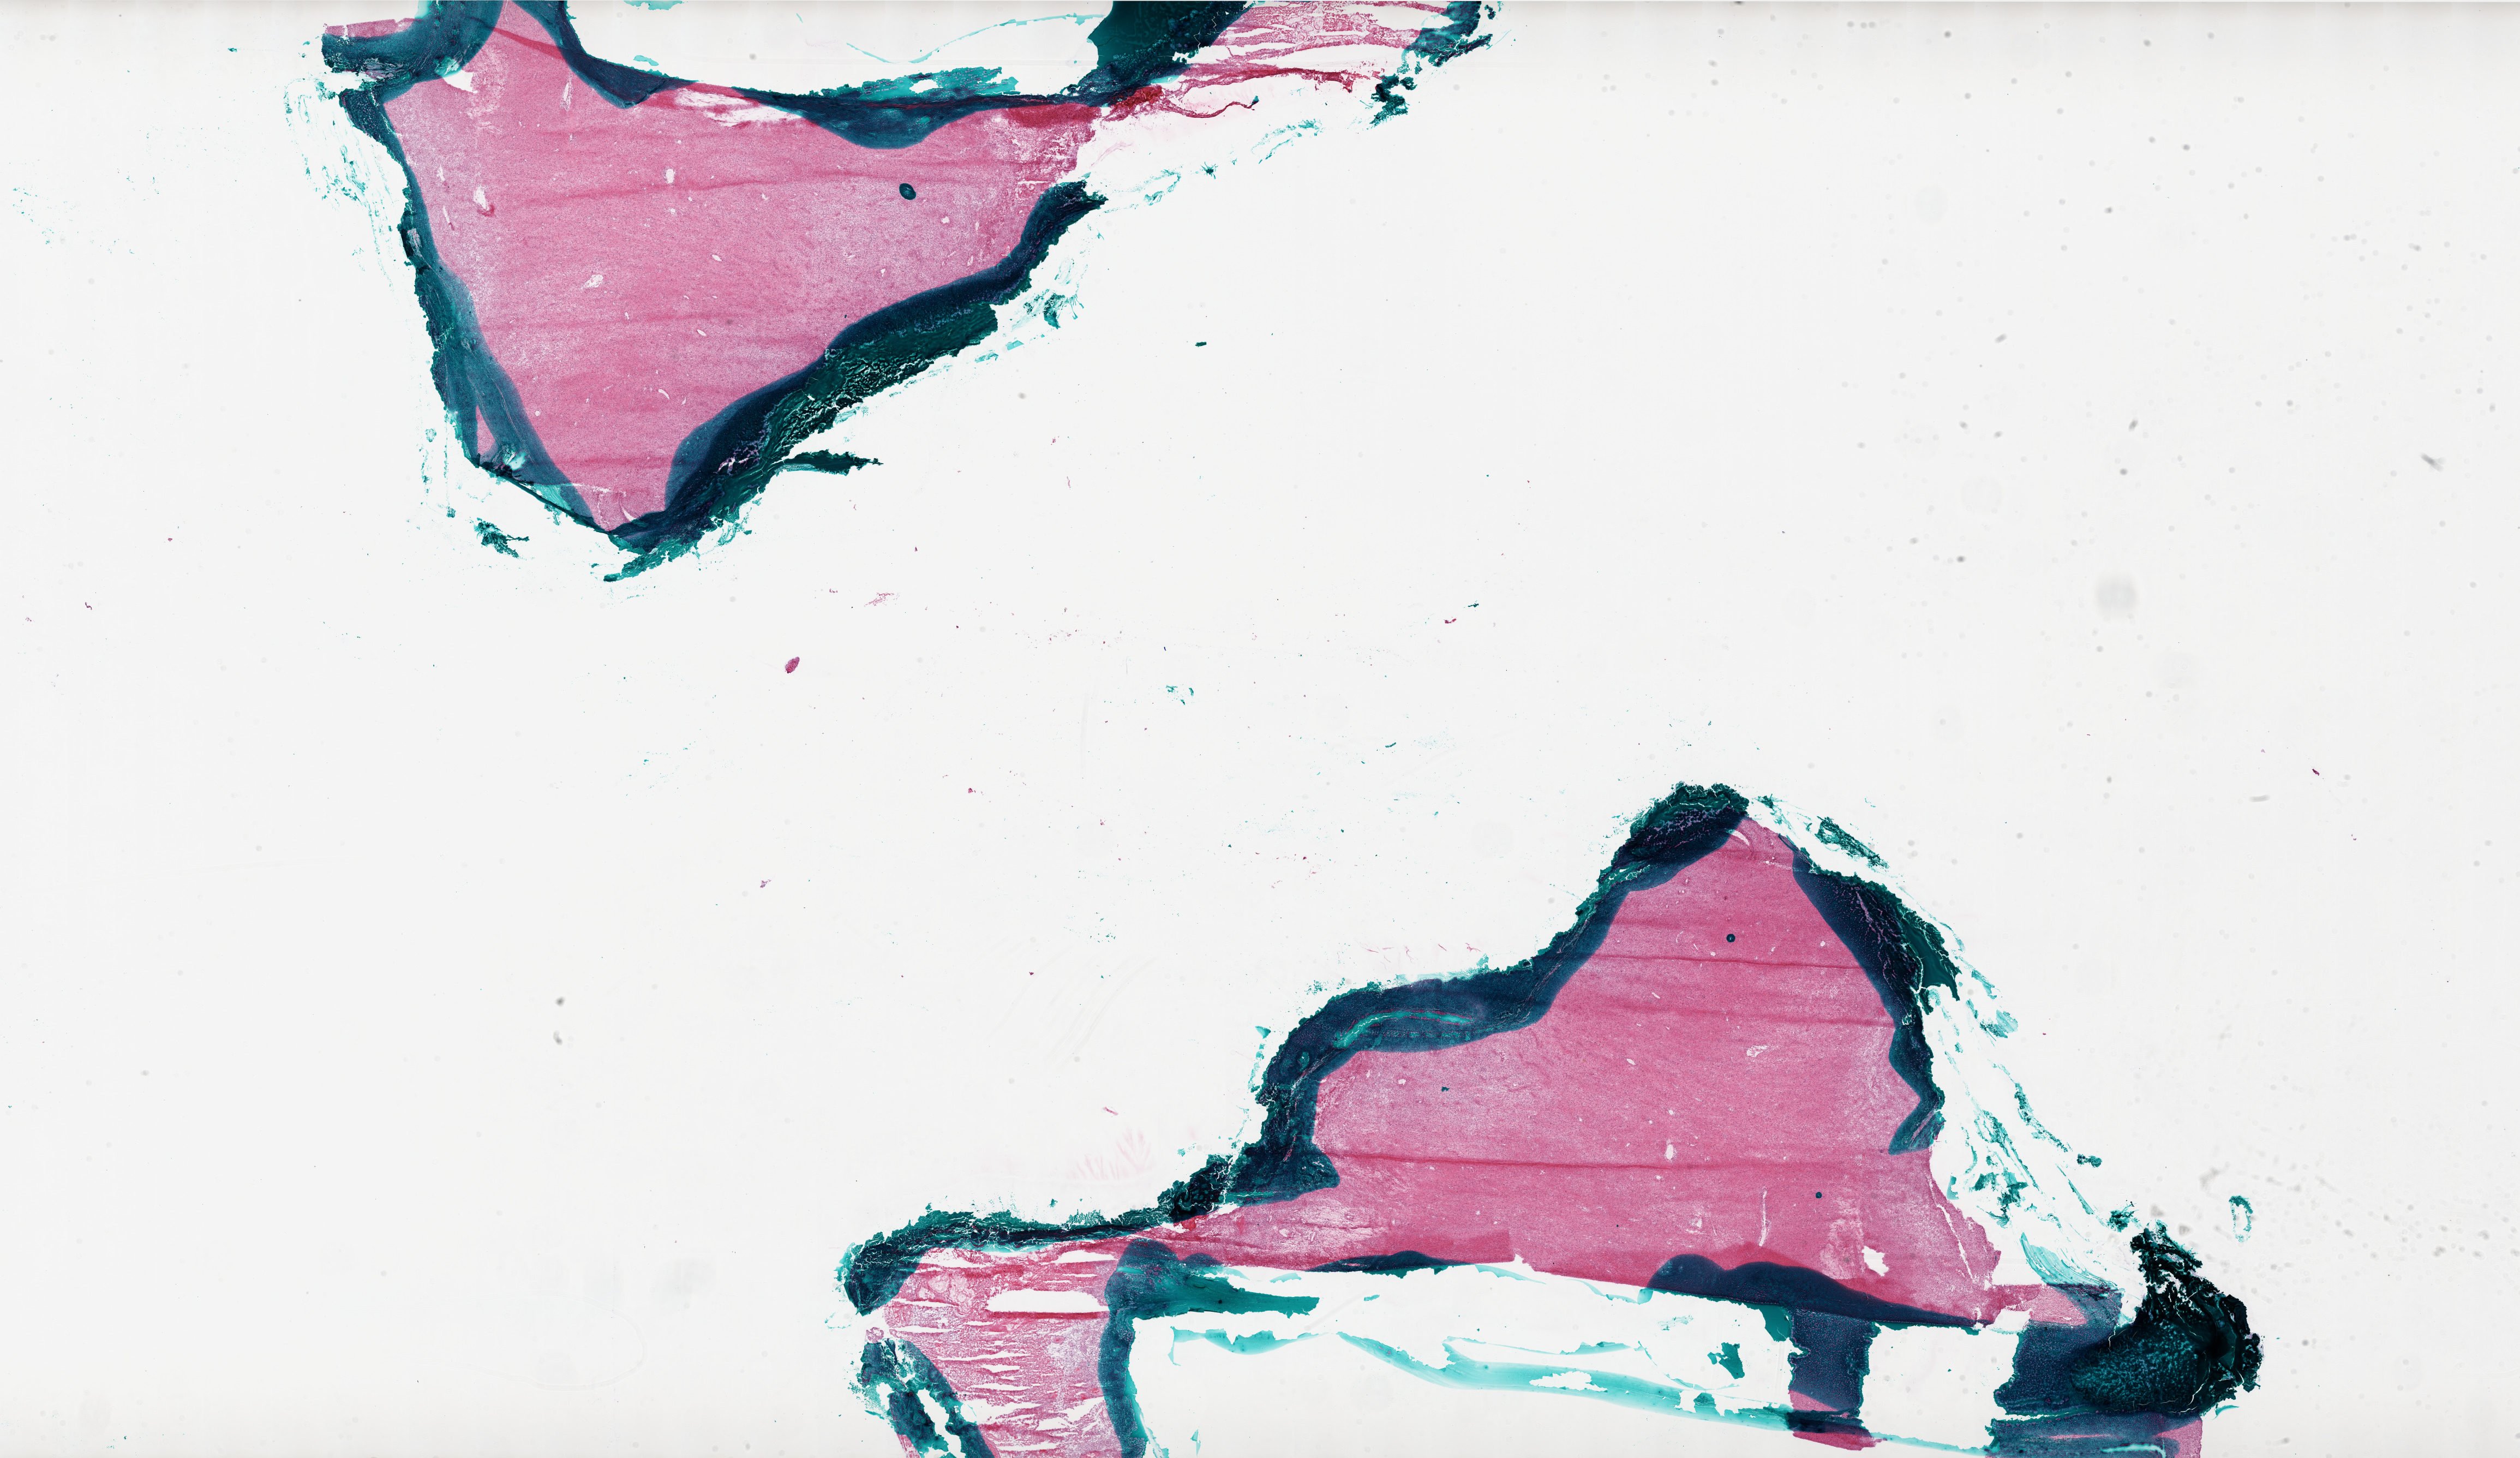
Whole-slide histology image, H&E — low-resolution overview of the scanned area, about 37.0 x 21.4 mm (acquisition: 20x scan); frozen section from the bottom of the tissue portion; primary tumour sample from the brain. Patient: female, age at initial diagnosis 33 years. Slide review estimates, as recorded: tumour cells 100%, tumour nuclei 100%, normal cells 0%, stromal cells 0%, necrosis 5%.
- pathologic diagnosis: Glioblastoma